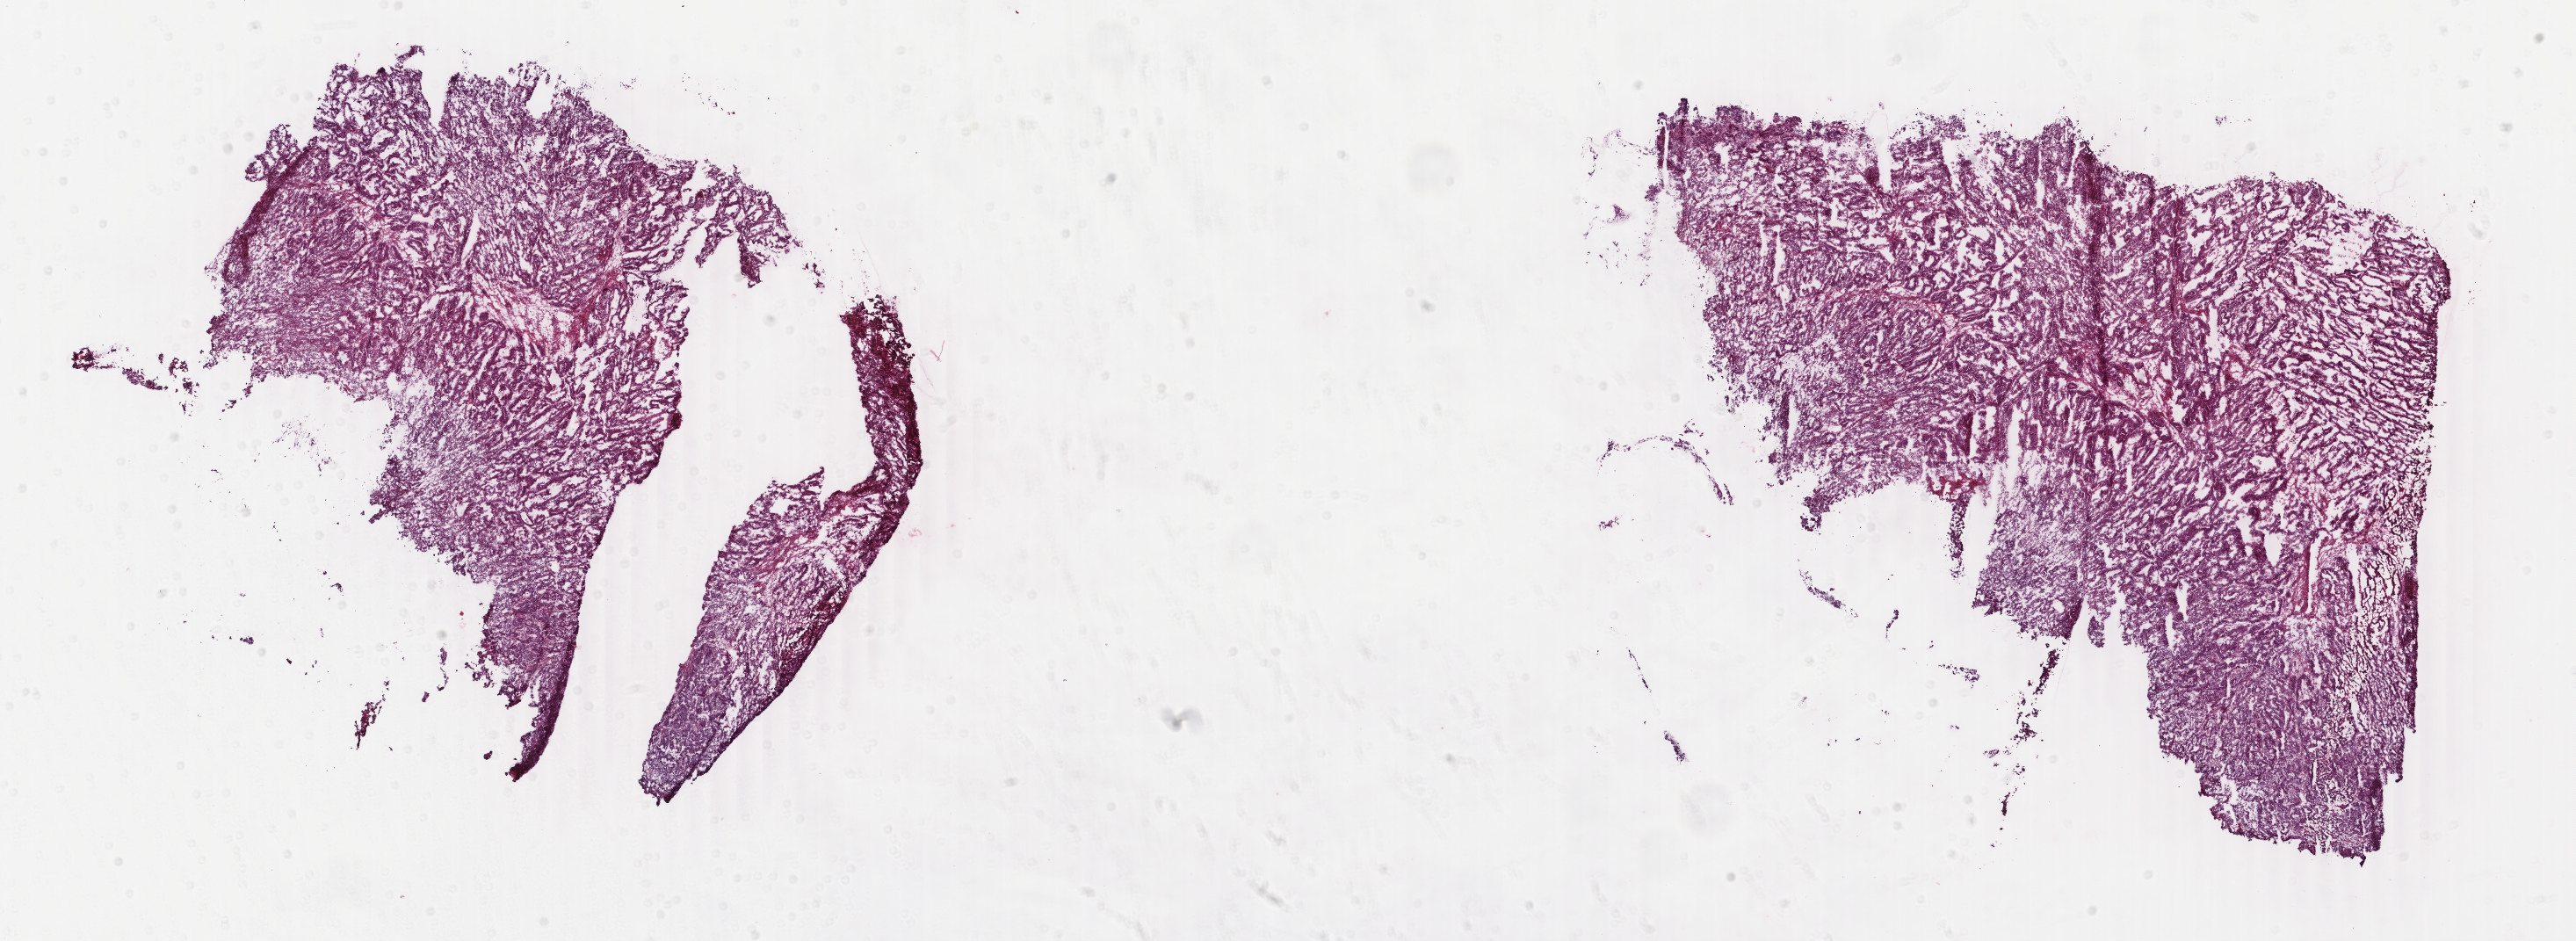
Whole-slide histology image, H&E — a low-resolution overview of the entire scanned area, about 23.3 x 8.5 mm (acquisition: 40x scan), frozen section, sample: primary tumour, uterus. Female, age 81 years at initial diagnosis. Histologic grade: G2 (moderately differentiated). Pathologist review of this section (percent, as recorded): tumour cells 80%, tumour nuclei 90%, normal cells 2%, stromal cells 3%, necrosis 15%. Inflammatory infiltration, as recorded: lymphocyte infiltration 0%, monocyte infiltration 0%, neutrophil infiltration 4%.
FIGO stage: IIA. Diagnosis: Endometrioid adenocarcinoma, NOS (endometrium).